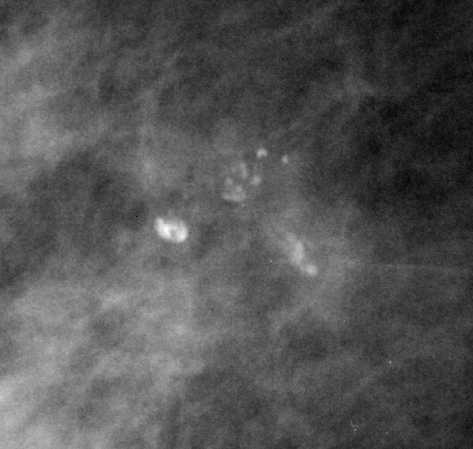
Region of interest cut from a scanned film mammogram (one marked finding), right breast, MLO view, BI-RADS breast density category 2 (scale 1–4).
Calcifications, morphology pleomorphic, distribution clustered; BI-RADS assessment category 4; subtlety rating 4 on a 1 (subtle) to 5 (obvious) scale; pathology result (as recorded, not read from the image): benign.